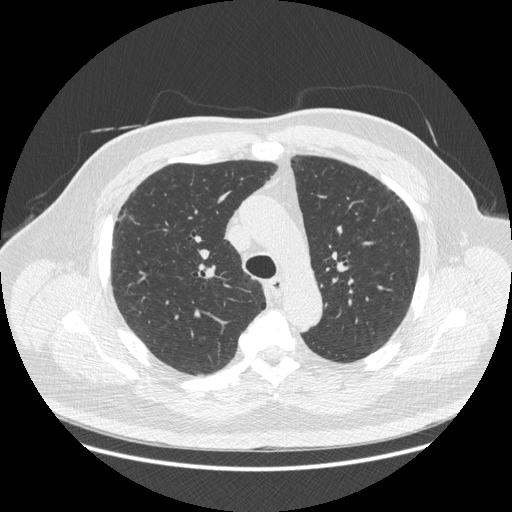
Chest CT (low-dose screening protocol), one axial image; baseline screening round; lung window (W 1500 / L -600 HU); standard (soft-tissue) reconstruction kernel (STANDARD); slice 82 of 266 in the series. Male, age 66 years at enrolment.
- Expert reader's lesion annotation, bounding box [x1, y1, x2, y2] px = [111, 205, 147, 234].
- Screening reader's record for this exam: no non-calcified nodule ≥4 mm recorded.
- Official screen result: negative screen, no significant abnormalities.
- Later outcome: lung cancer diagnosed 742 days after this screen (after the third annual screen) — non-small cell carcinoma, right upper lobe, stage IV (AJCC 6th edition), 50 mm at pathology.